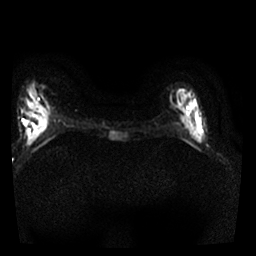
Breast MRI, one axial slice. Slice 7 of 25 in the series (ordered by position). Diffusion-weighted series; image 2 of 4 stored at this slice position (different b-values; order by instance number). 1.5 T. 4 mm slice thickness. 256 × 256 image matrix, field of view 300 × 300 mm. Female patient.
Annotated regions visible in this slice (outlined manually by an expert reader):
- tumour on diffusion-weighted imaging: bounding box [x1, y1, x2, y2] px = [178, 99, 204, 144]